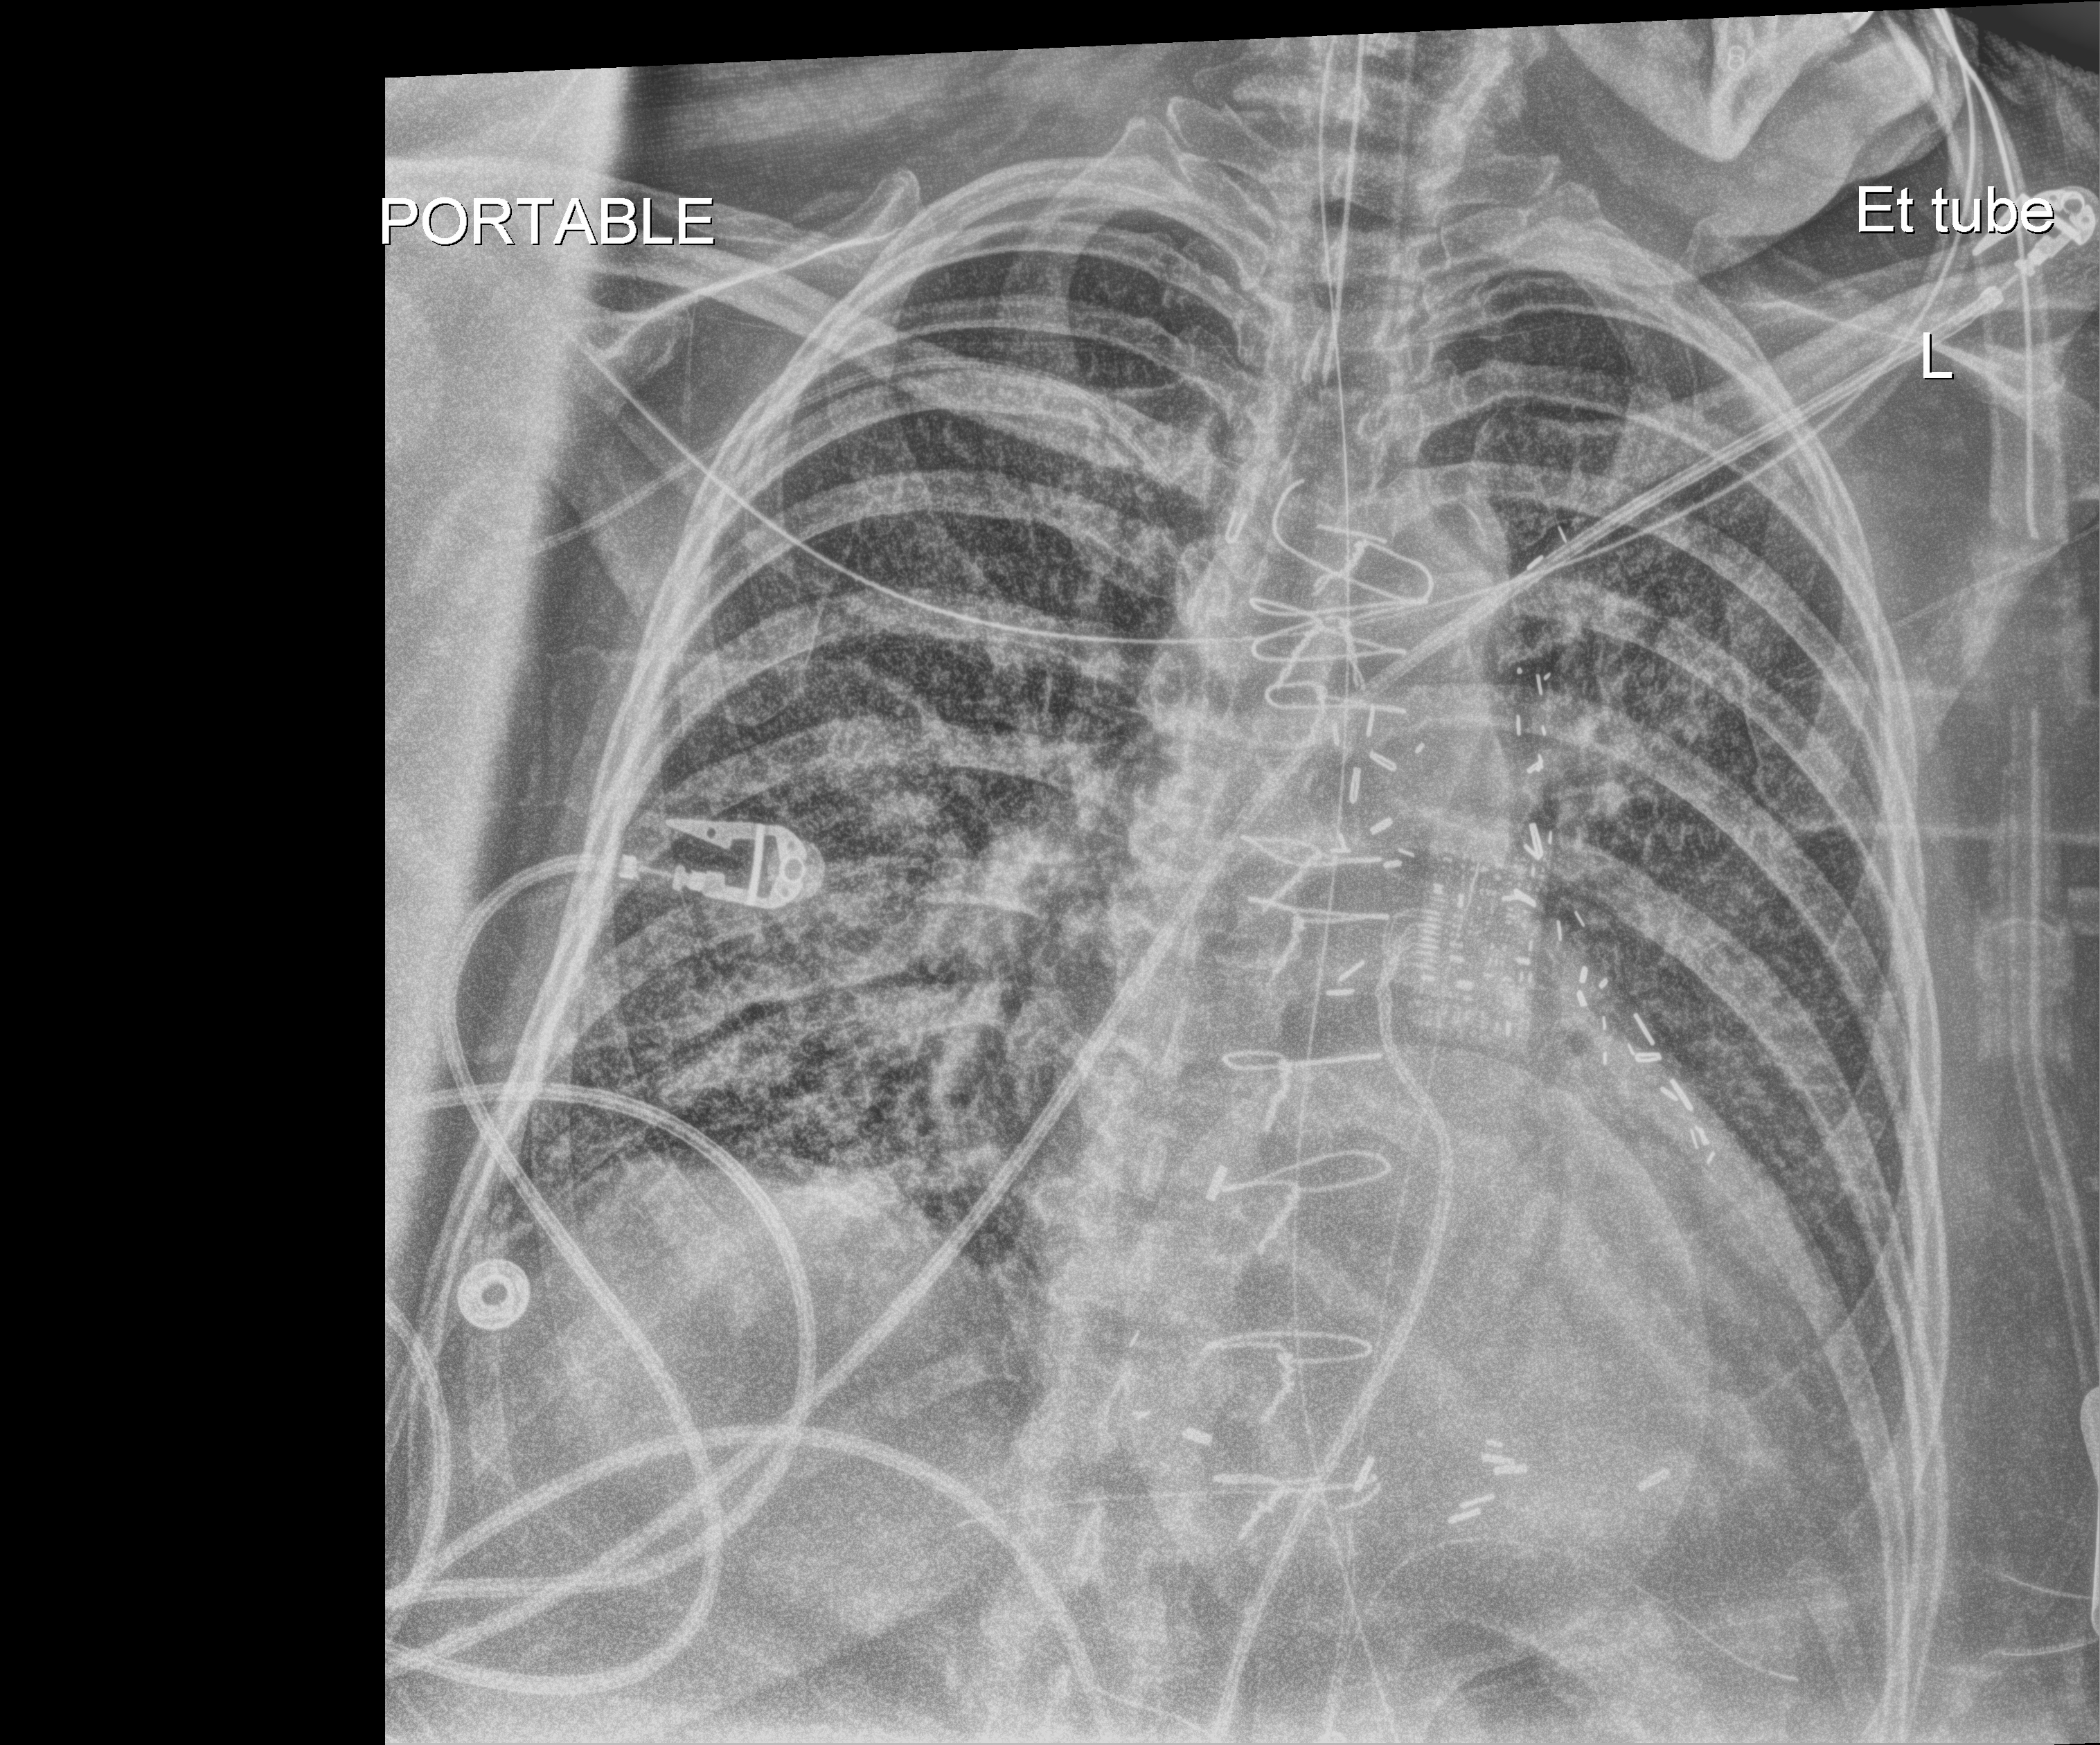
Bedside chest radiograph (digital radiography), anteroposterior (AP) projection. Female patient hospitalised with COVID-19, age 60–74 years.
Hospital-stay facts (about this admission, not read from this image; timing relative to this image not recorded): mechanically ventilated during this hospital stay: yes; length of hospital stay: 25 days.